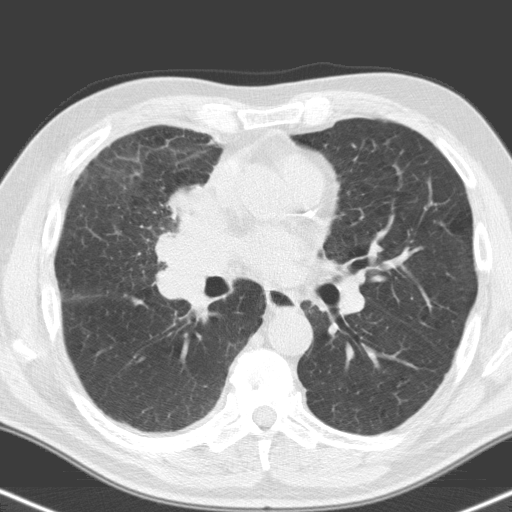
Low-dose screening chest CT, one axial slice; slice 87 of 160 in the series (ordered by position); 120 kVp; lung window (W 1500 / L -600 HU); 512 × 512 image matrix, field of view 324 × 324 mm.
Structures marked on this image (manually delineated by an expert):
- lesion 1 (tumor, hilum of right lung): bounding box [x1, y1, x2, y2] px = [158, 188, 240, 309]